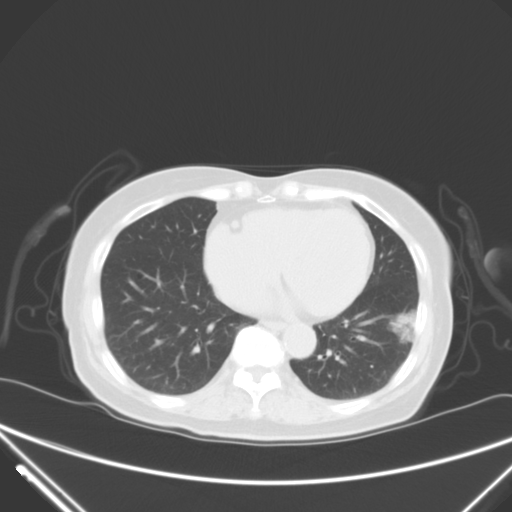
Chest CT, one axial slice; slice 22 of 62 in the series (ordered by position); 120 kVp; lung window (W 1500 / L -600 HU); 512 × 512 image matrix, field of view 377 × 377 mm. Female patient, age 82 years. From the clinical record (not read from this slice): clinical TNM (as recorded): T1c N0 M0.
Annotated regions visible in this slice (bounding box drawn by a radiologist):
- lung tumour (recorded histology: adenocarcinoma): bounding box (x1, y1, x2, y2) in pixels: (390, 306, 428, 350)